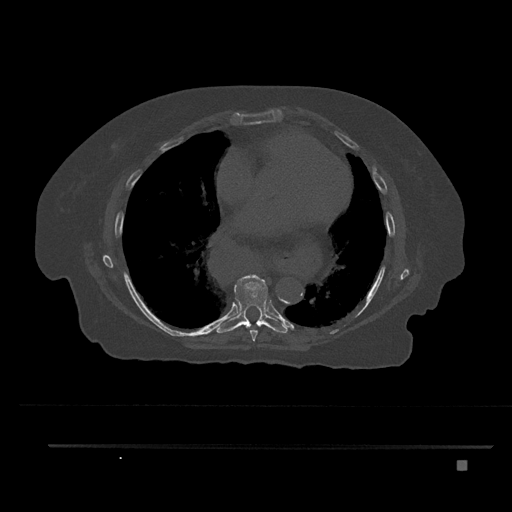
CT including the spine, one axial slice. Slice 456 of 797 in the series (ordered by position). Reconstruction kernel Br40s/3. 120 kVp. Bone window (W 1800 / L 400 HU). 512 × 512 image matrix, field of view 437 × 437 mm. Female patient, age 76 years. From the clinical record (not read from this slice): primary cancer: lung.
Annotated regions visible in this slice (semi-automatic segmentation, software-assisted and operator-edited):
- T7 vertebra: box from (x=249, y=328) to (x=258, y=341) px
- T8 vertebra: (x=217, y=275)–(x=288, y=333)